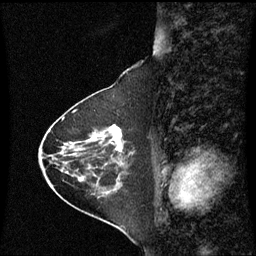
Breast MRI (dynamic contrast-enhanced), one sagittal slice. Slice 25 of 60 in the series (ordered by position). Dynamic contrast-enhanced series, image 2 of 3 at this slice position (ordered by acquisition). 1.5 T. TE 4.2 ms, TR 8.9 ms. 256 × 256 image matrix, field of view 210 × 210 mm. Patient: female, 63 years. Case-level facts recorded for this patient, not image findings: setting: breast cancer imaged before/during neoadjuvant chemotherapy; receptor status: HR-positive, HER2-negative.
Annotated regions visible in this slice (semi-automatically segmented with operator editing):
- analysis volume of interest (the breast-tissue region the enhancement analysis was run in; not a lesion): box from (x=88, y=126) to (x=125, y=163) px
- tumour enhancement mask (voxels above the 70 % enhancement threshold inside the analysis volume of interest): (x=95, y=126)–(x=123, y=152)